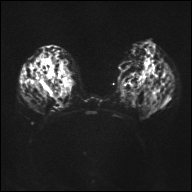
Breast MRI, one axial slice; diffusion-weighted series; image 2 of 4 stored at this slice position (different b-values; order by instance number); 1.5 T; 4 mm slice thickness; 192 × 192 image matrix. Female patient.
Outlined on this slice (outlined manually by an expert reader):
- tumour on diffusion-weighted imaging: bounding box <37,72,61,97> (left, top, right, bottom; pixels)